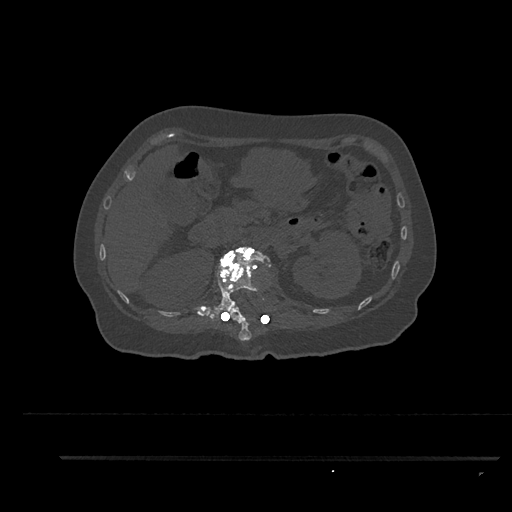
CT including the spine, one axial slice; position 231 of 797 along the scan axis; bone window (W 1800 / L 400 HU); 512 × 512 image matrix, field of view 408 × 408 mm. Patient: female, 44 years. From the clinical record (not read from this slice): primary cancer: renal; vertebrae with lytic lesions (as recorded): L1.
Structures marked on this image (semi-automatically segmented with operator editing):
- L1 vertebra: box from (x=208, y=246) to (x=272, y=322) px
- T12 vertebra: (x=220, y=308)–(x=253, y=341)